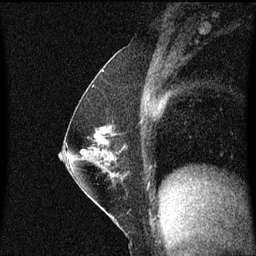
Breast MRI (dynamic contrast-enhanced), one sagittal slice; position 30 of 60 along the scan axis; dynamic contrast-enhanced series, image 2 of 3 at this slice position (ordered by acquisition); 1.5 T; TE 4.2 ms, TR 8.4 ms; 2 mm slice thickness; 256 × 256 image matrix. Patient: female, 52 years. Case-level facts recorded for this patient, not image findings: setting: breast cancer imaged before/during neoadjuvant chemotherapy; receptor status: HER2-positive.
Structures marked on this image (semi-automatic segmentation, software-assisted and operator-edited):
- analysis volume of interest (the breast-tissue region the enhancement analysis was run in; not a lesion): box from (x=71, y=118) to (x=129, y=187) px
- tumour enhancement mask (voxels above the 70 % enhancement threshold inside the analysis volume of interest): (x=98, y=128)–(x=109, y=143)